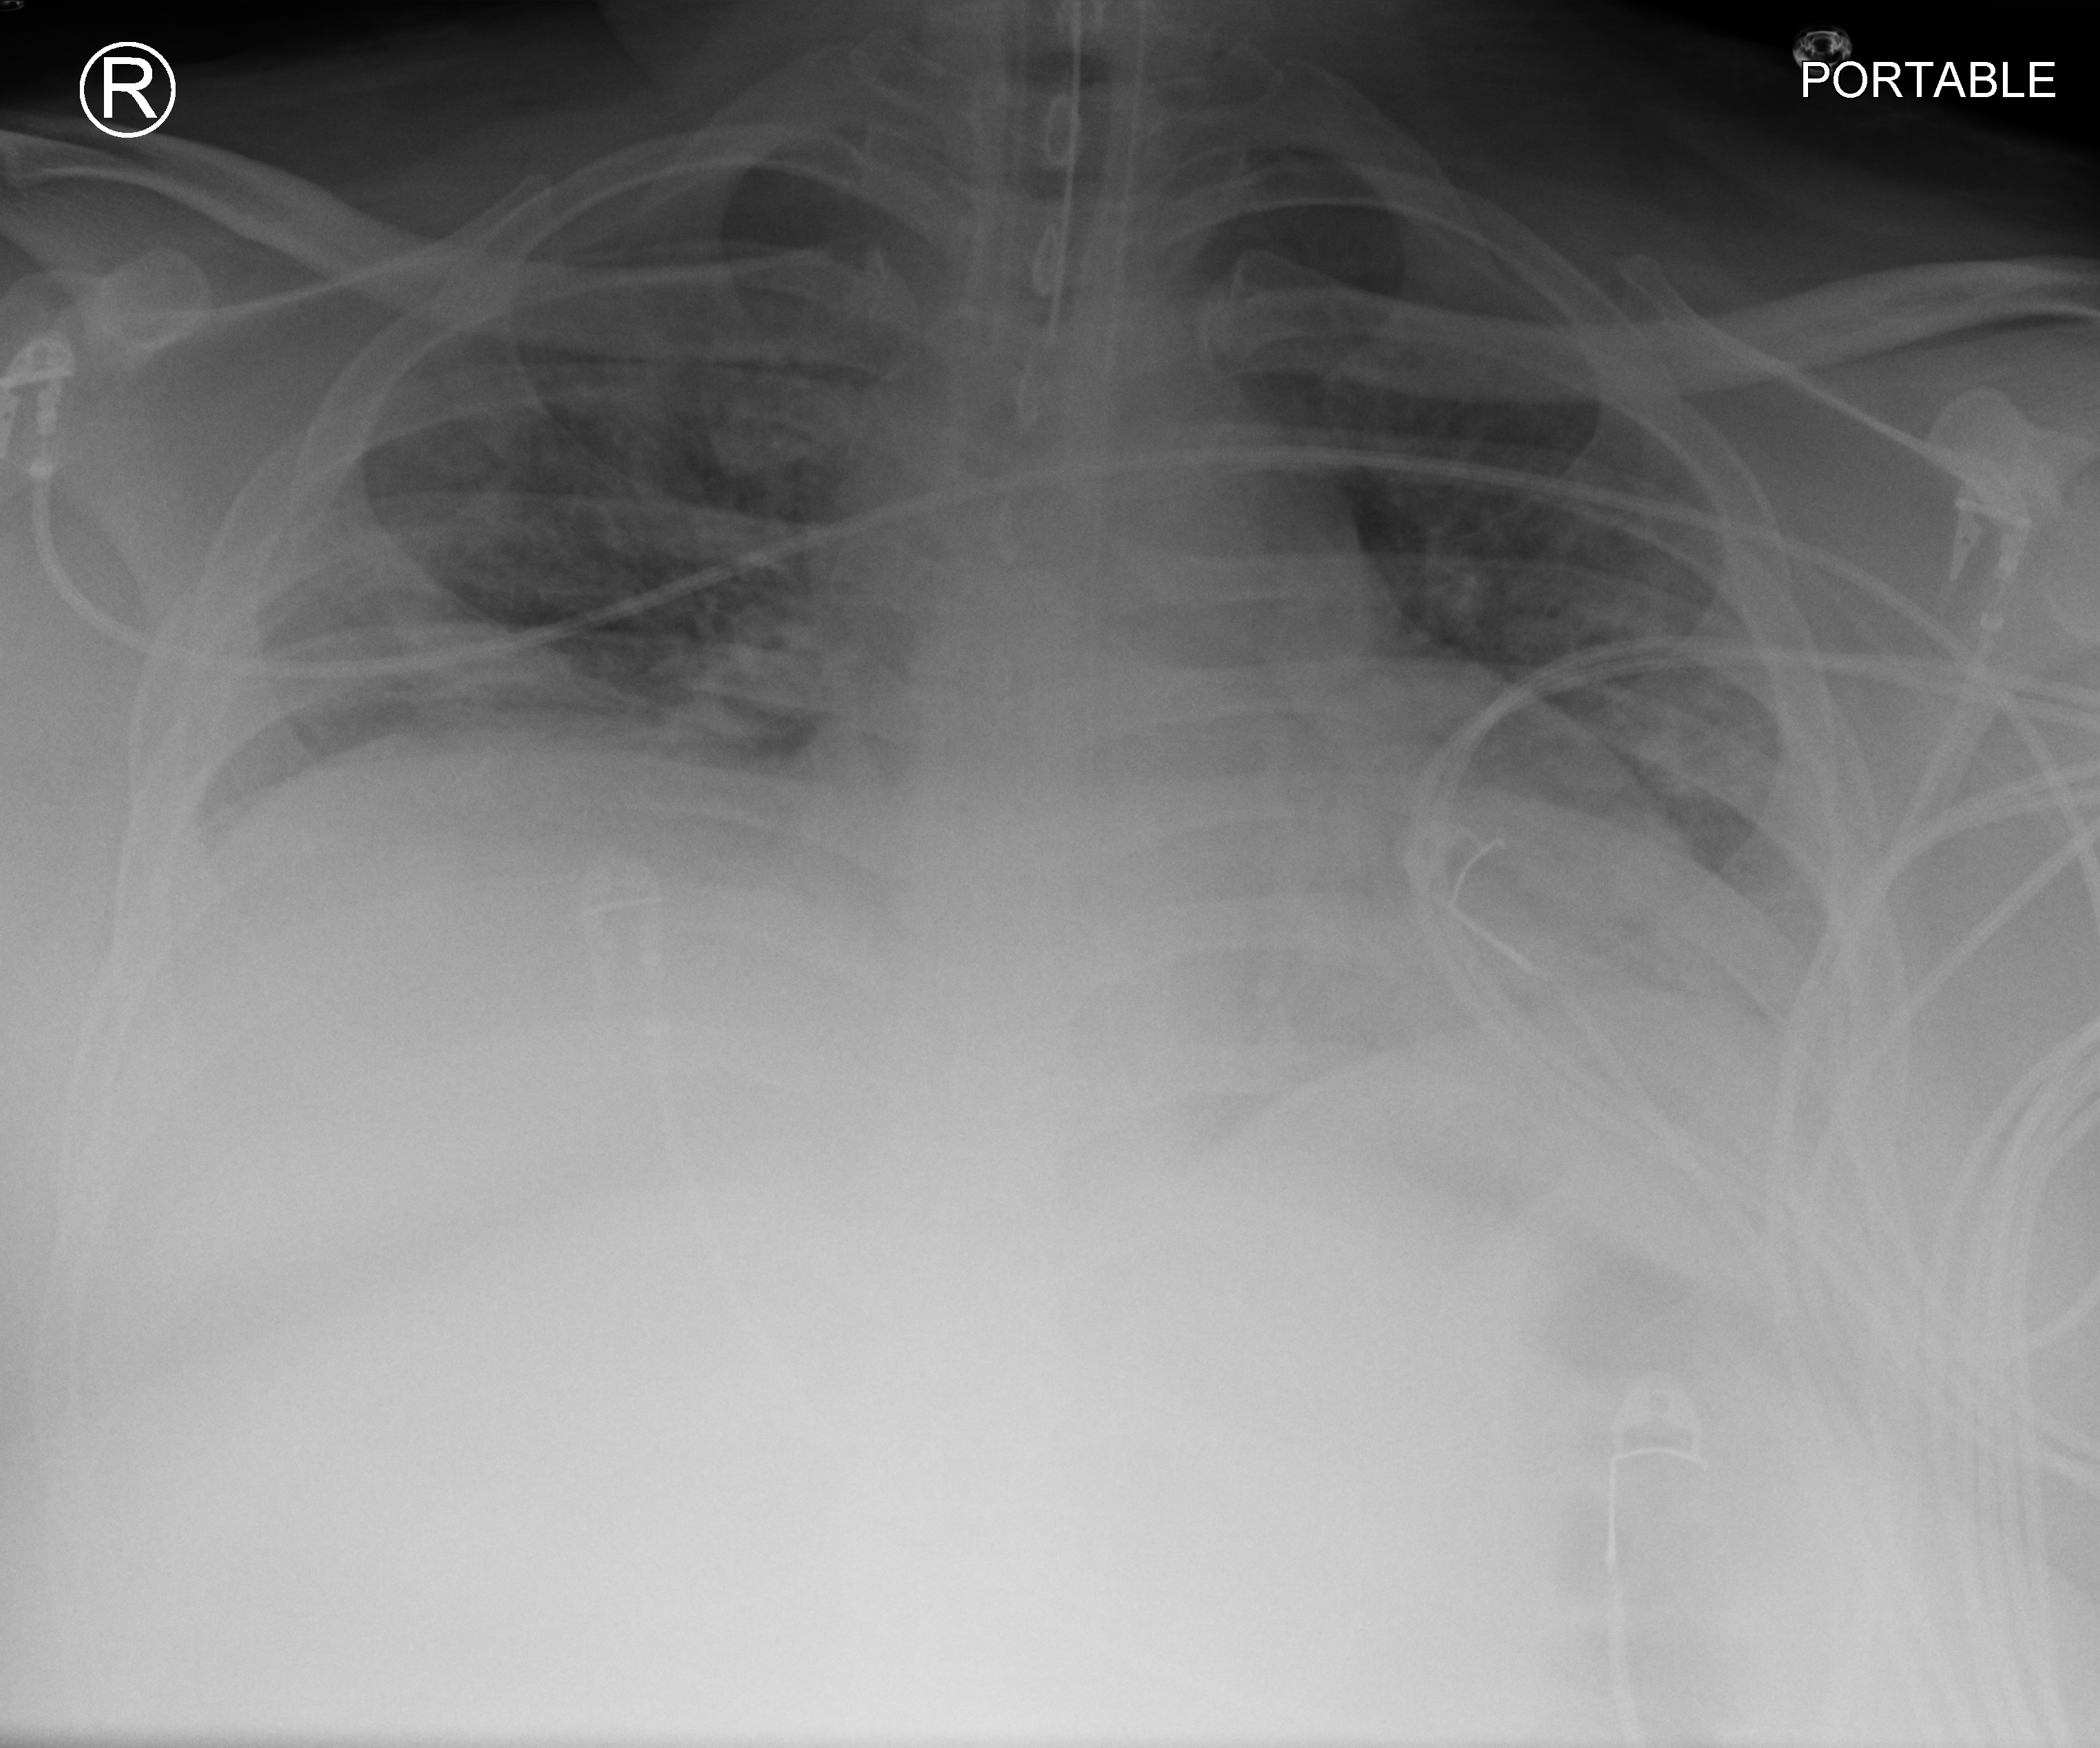
Portable chest radiograph; anteroposterior (AP) projection. Male patient hospitalised with COVID-19, age 18–59 years.
Admission-level facts for this patient (not findings on this image; timing relative to this image not recorded): admitted to intensive care during this hospital stay: yes; COPD (admission record): yes; other chronic lung disease (admission record): yes.